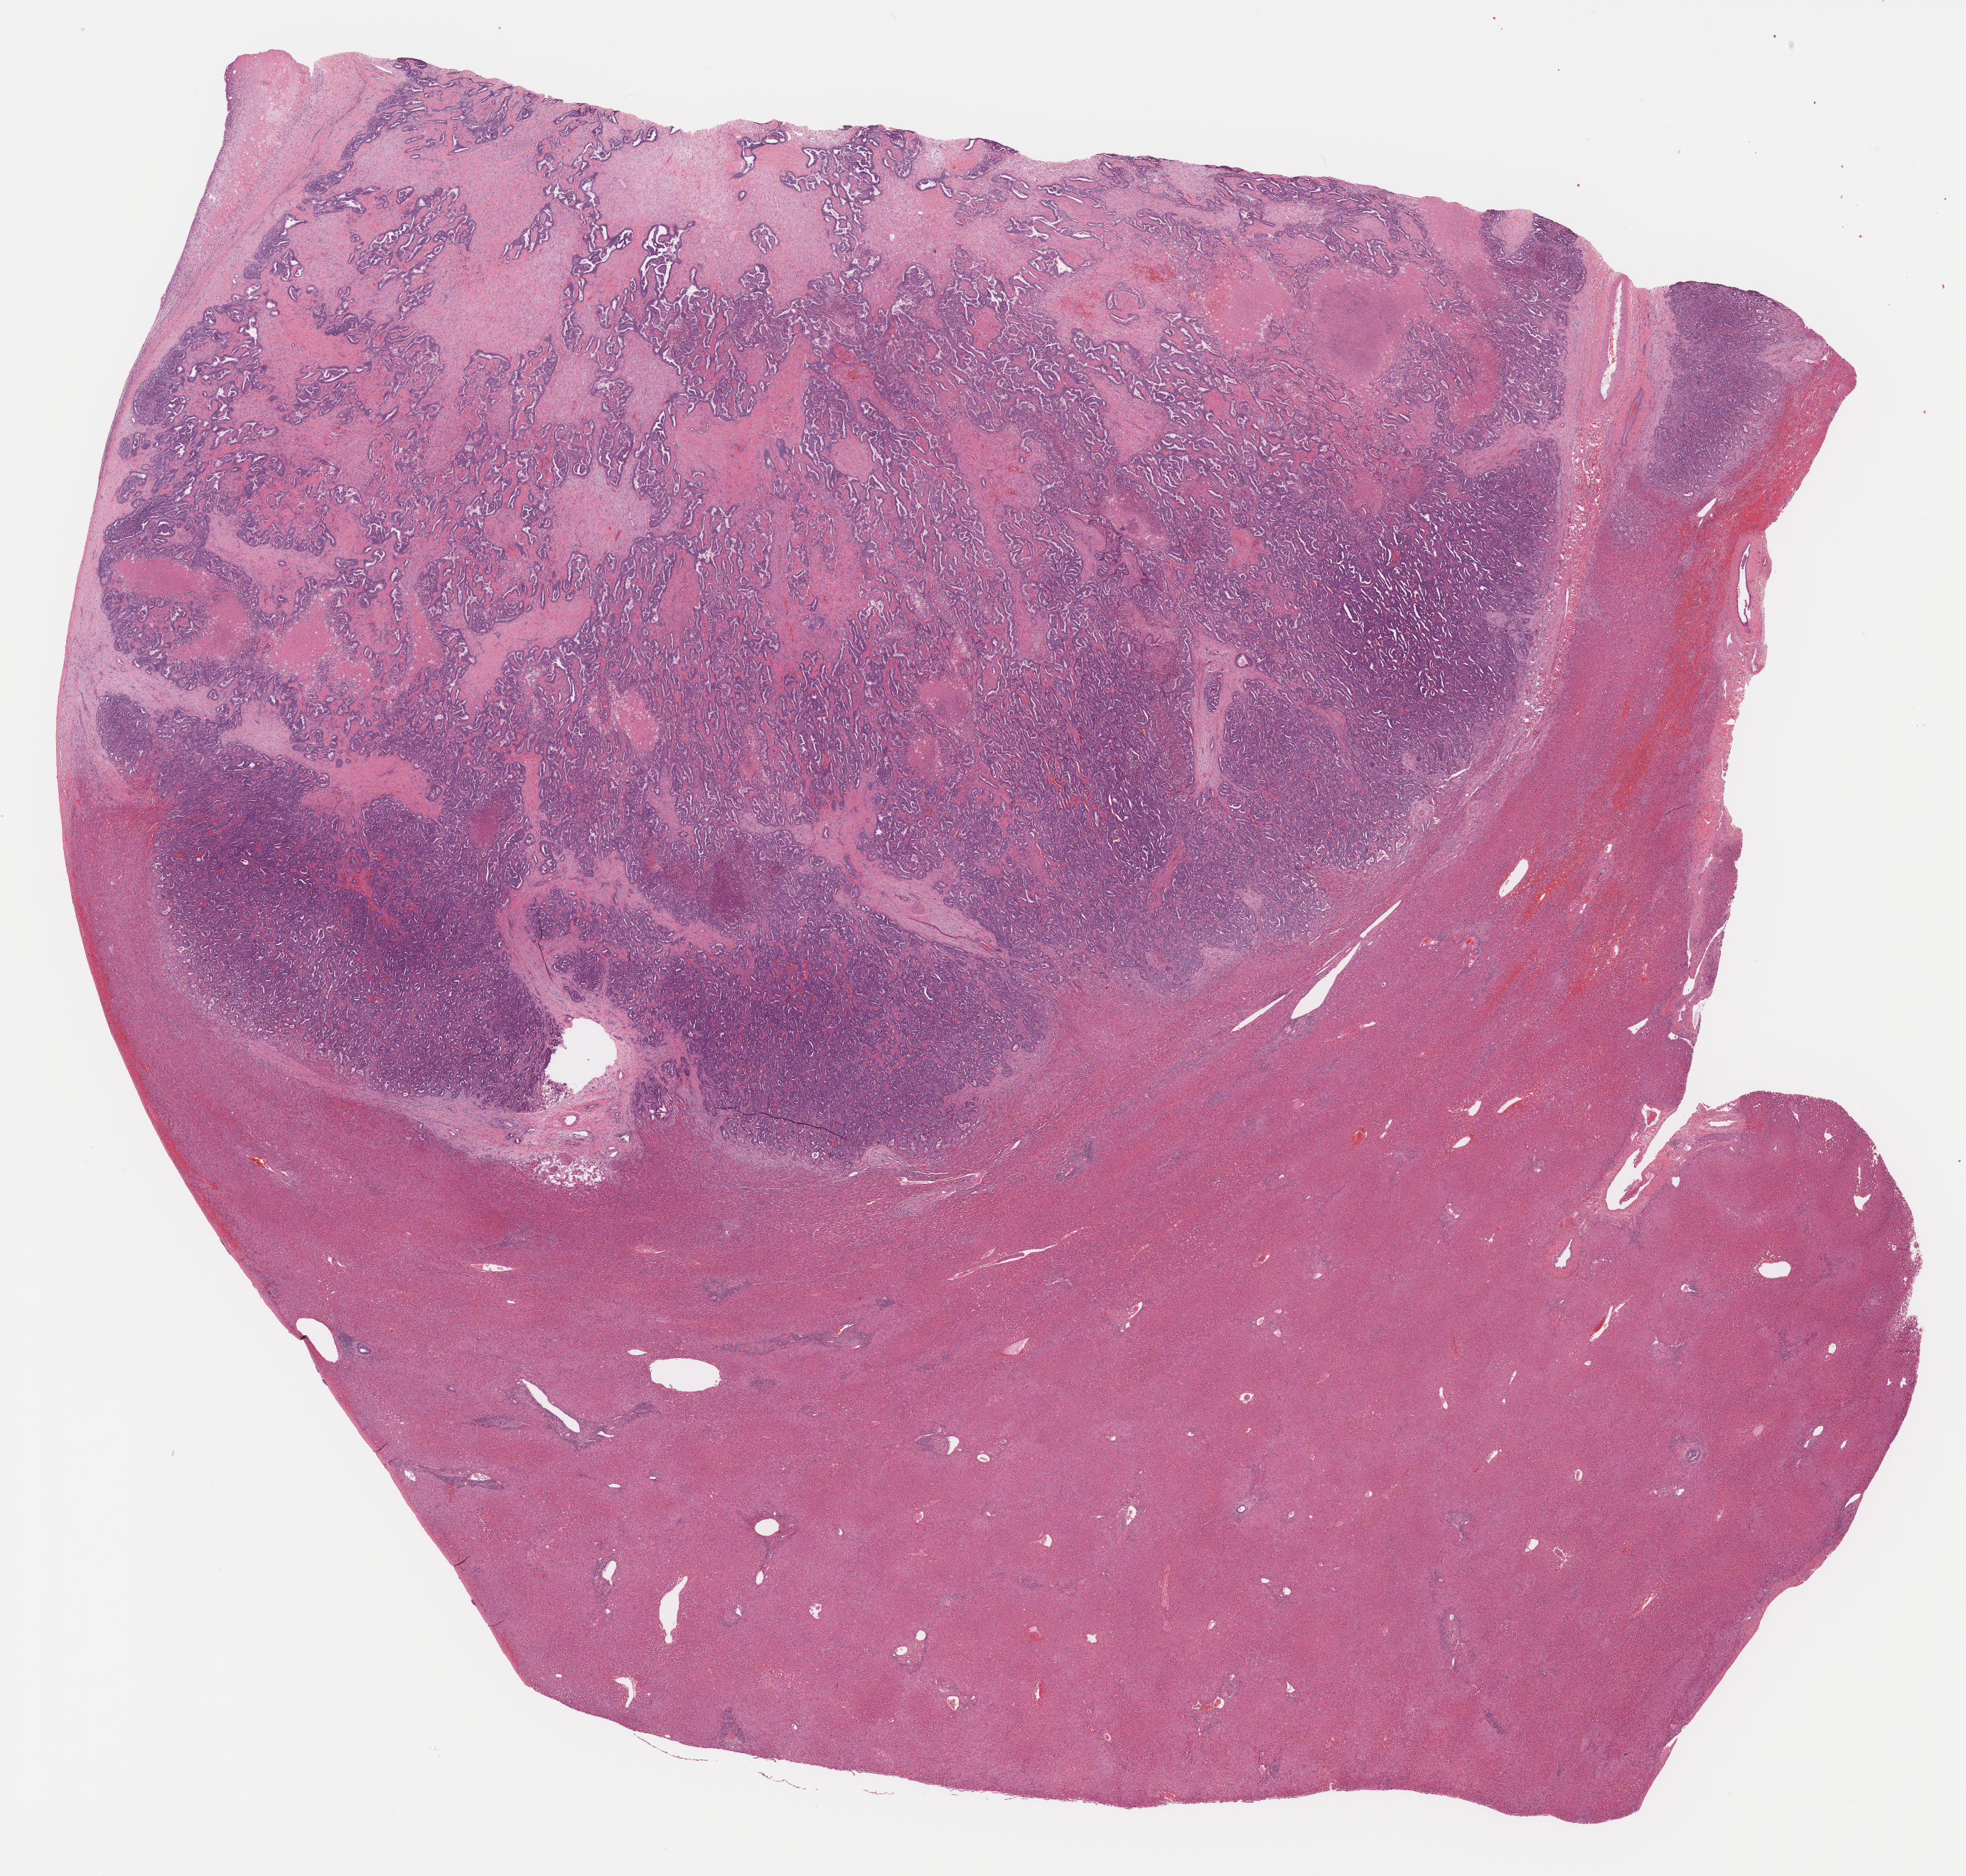
Digitized H&E tissue section (whole slide), low-resolution overview of the scanned area, about 22.4 x 21.4 mm (from a 40x scan). Formalin-fixed paraffin-embedded (FFPE) diagnostic section. Primary tumour sample from the bile duct. Female, age 64 years at initial diagnosis.
Histologic diagnosis: Cholangiocarcinoma (intrahepatic bile duct).